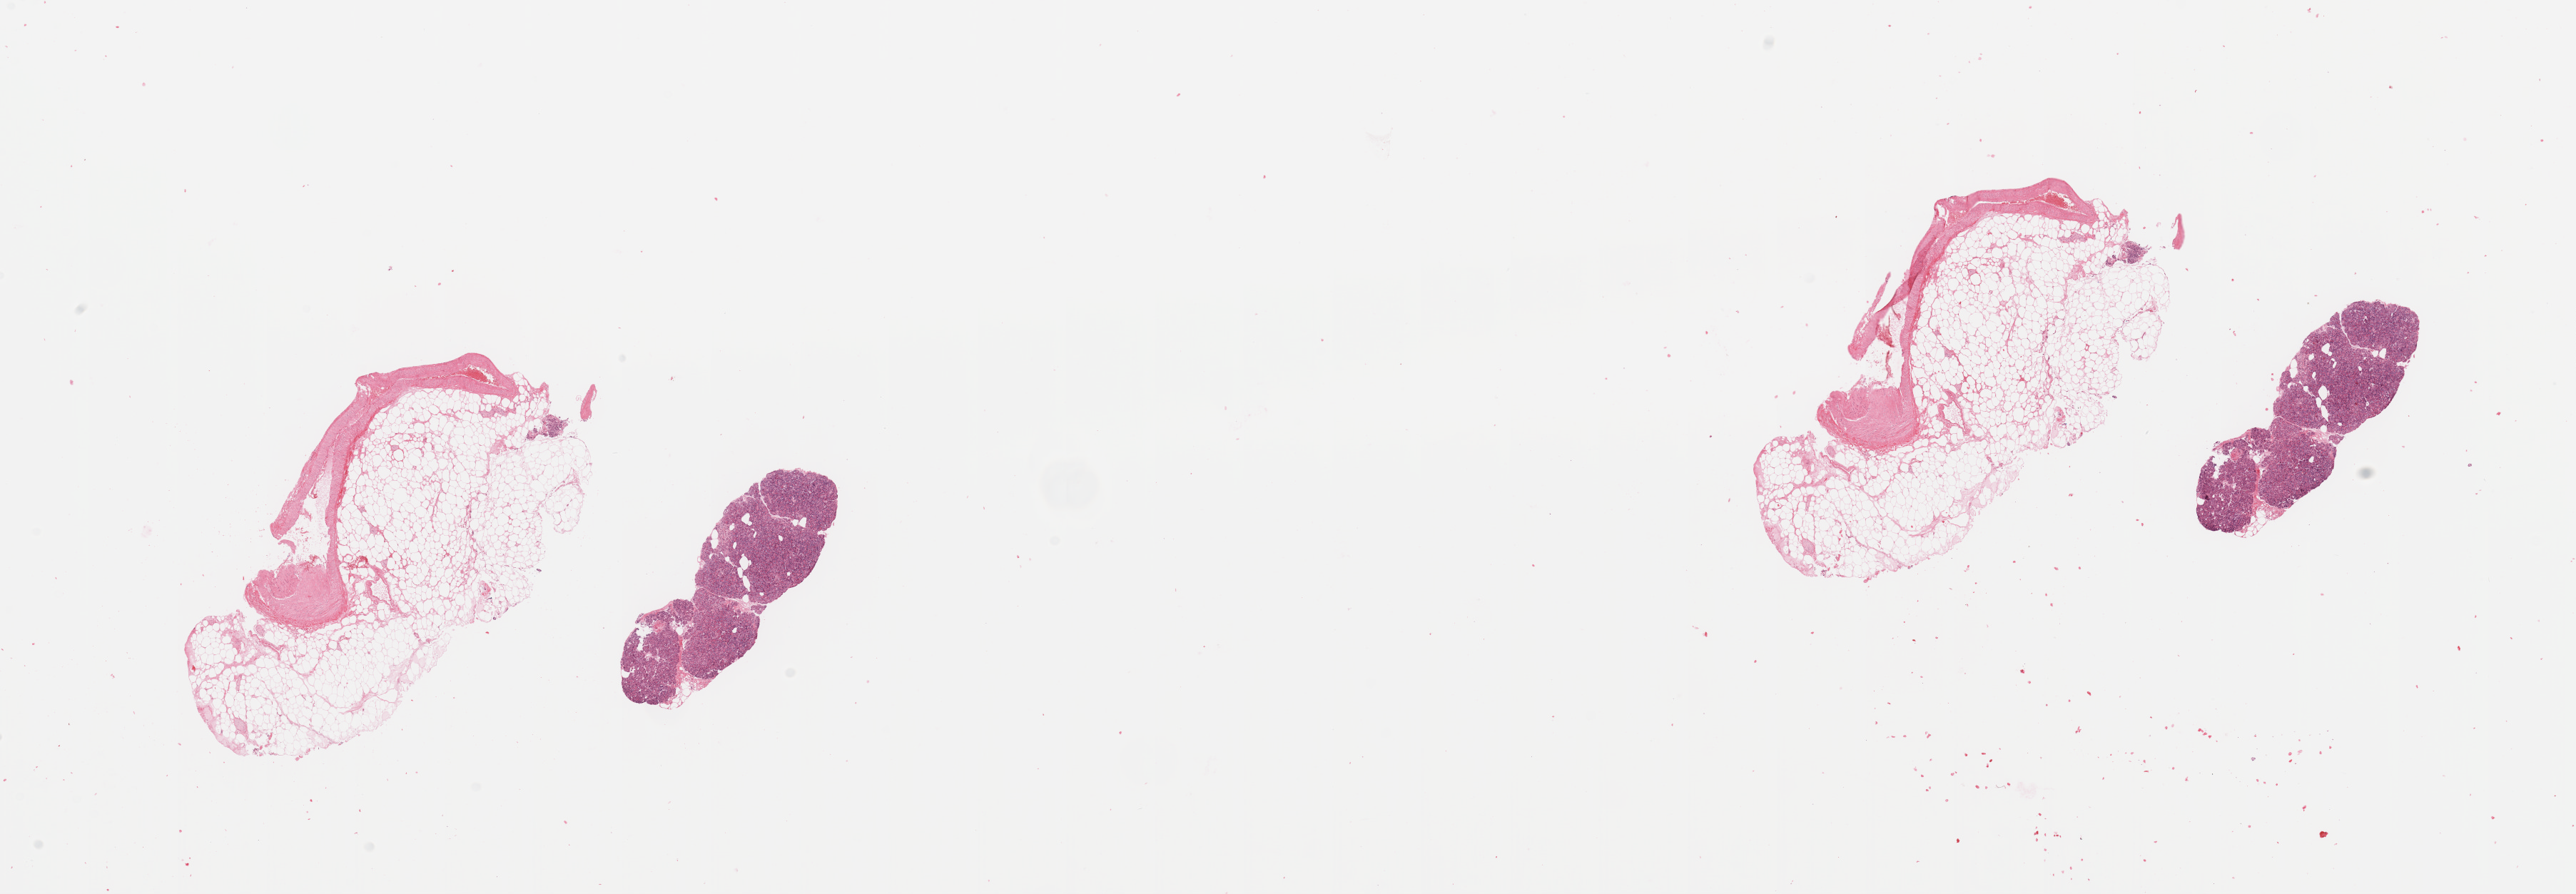
Digitized H&E tissue section (whole slide), low-resolution overview of the scanned area, about 28.5 x 9.9 mm; normal (non-tumour) tissue sample, pancreas. Patient: male, age 75 years.
This section: normal (non-tumour) tissue from the same patient. Patient diagnosis: Infiltrating duct carcinoma, NOS.